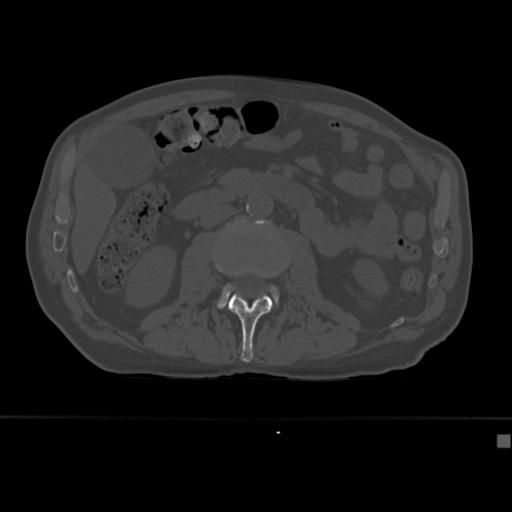
CT including the spine, one axial slice; position 141 of 430 along the scan axis; reconstruction kernel Br40s; 120 kVp; bone window (W 1800 / L 400 HU); 512 × 512 image matrix, field of view 337 × 337 mm. Male patient, age 64 years. From the clinical record (not read from this slice): primary cancer: uterus.
Annotated regions visible in this slice (semi-automatic segmentation, software-assisted and operator-edited):
- L2 vertebra: bounding box [x1, y1, x2, y2] px = [228, 264, 288, 363]
- L3 vertebra: [217, 219, 279, 309]